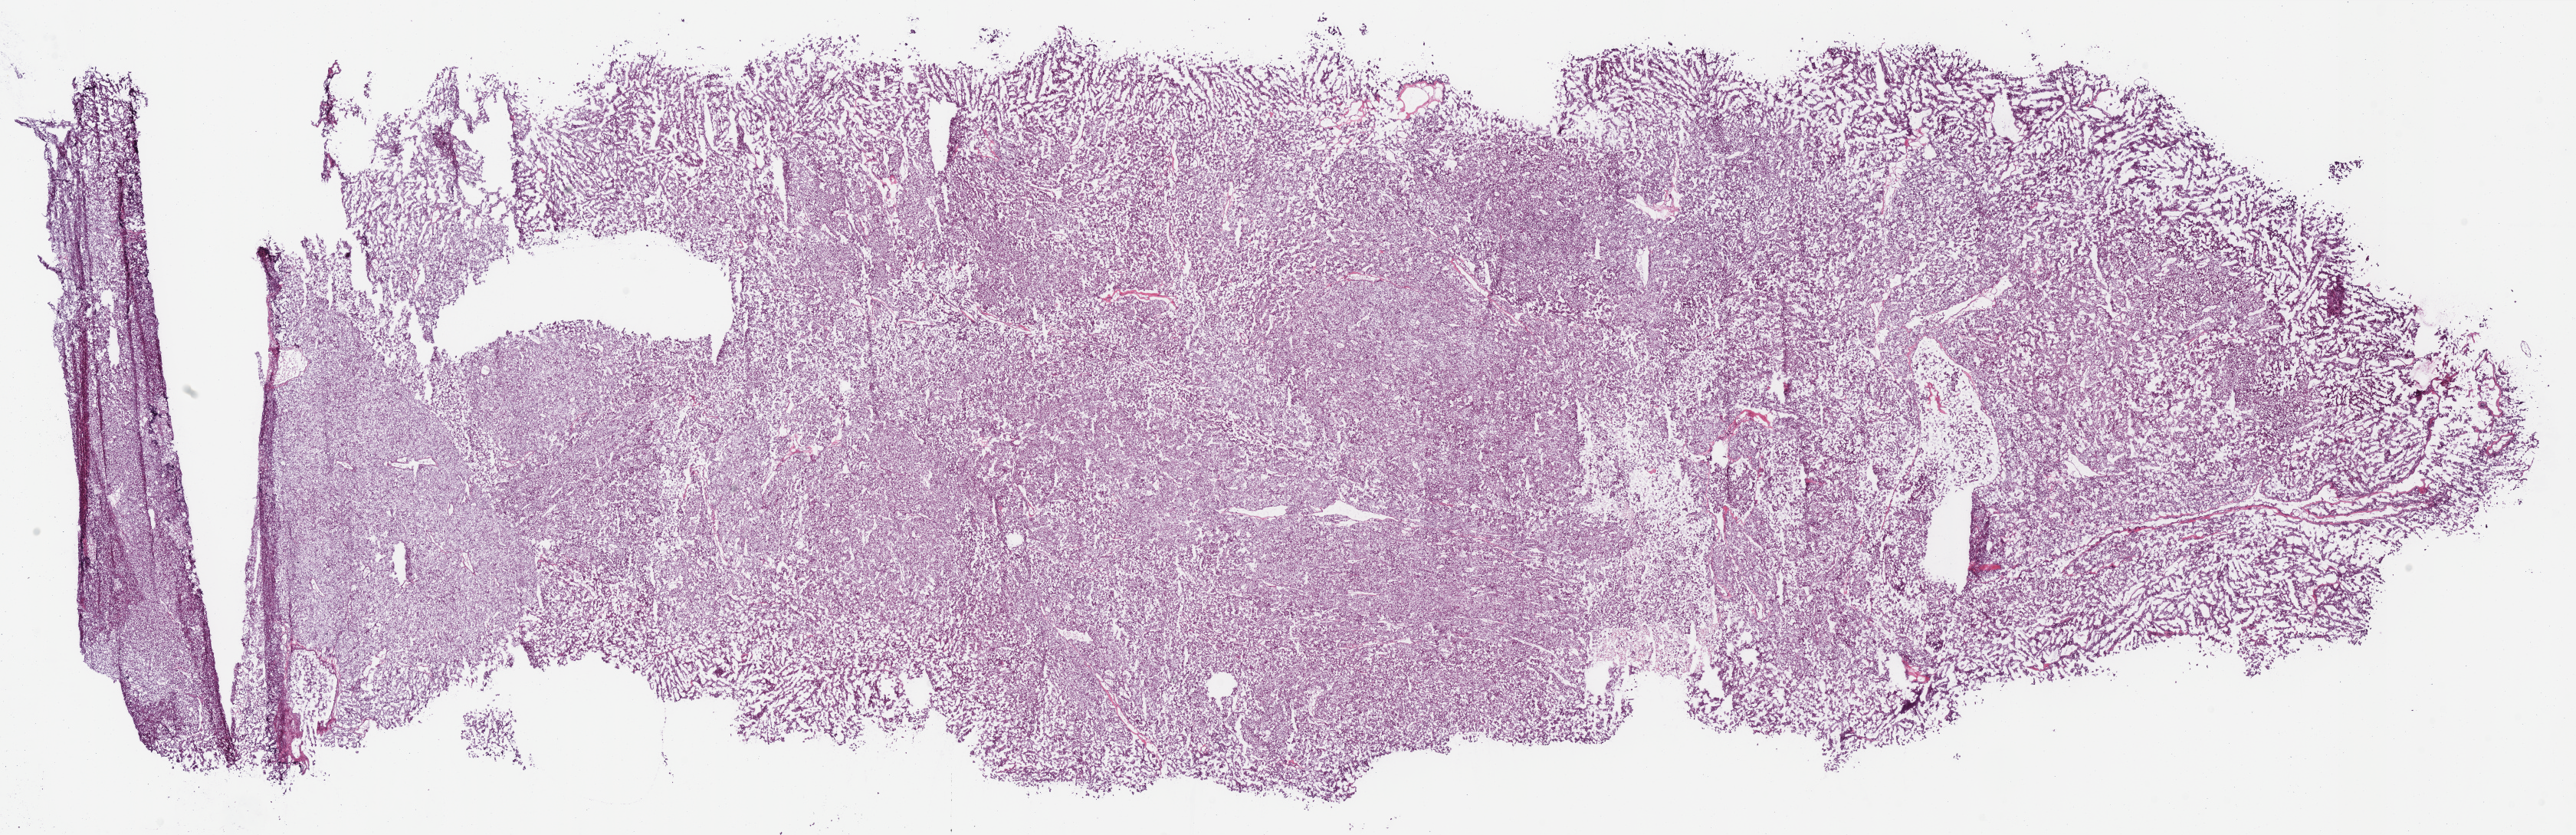
Hematoxylin and eosin (H&E) stained whole-slide image, whole scanned area (about 26.4 x 8.6 mm) shown as a low-resolution overview; frozen section; kidney, primary tumour sample. Female patient; age at initial diagnosis 50 years. Slide review estimates, as recorded: tumour cells 90%, tumour nuclei 90%, normal cells 0%, stromal cells 10%, necrosis 0%.
• AJCC pathologic stage: II (7th edition)
• pathologic diagnosis: Renal cell carcinoma, chromophobe type